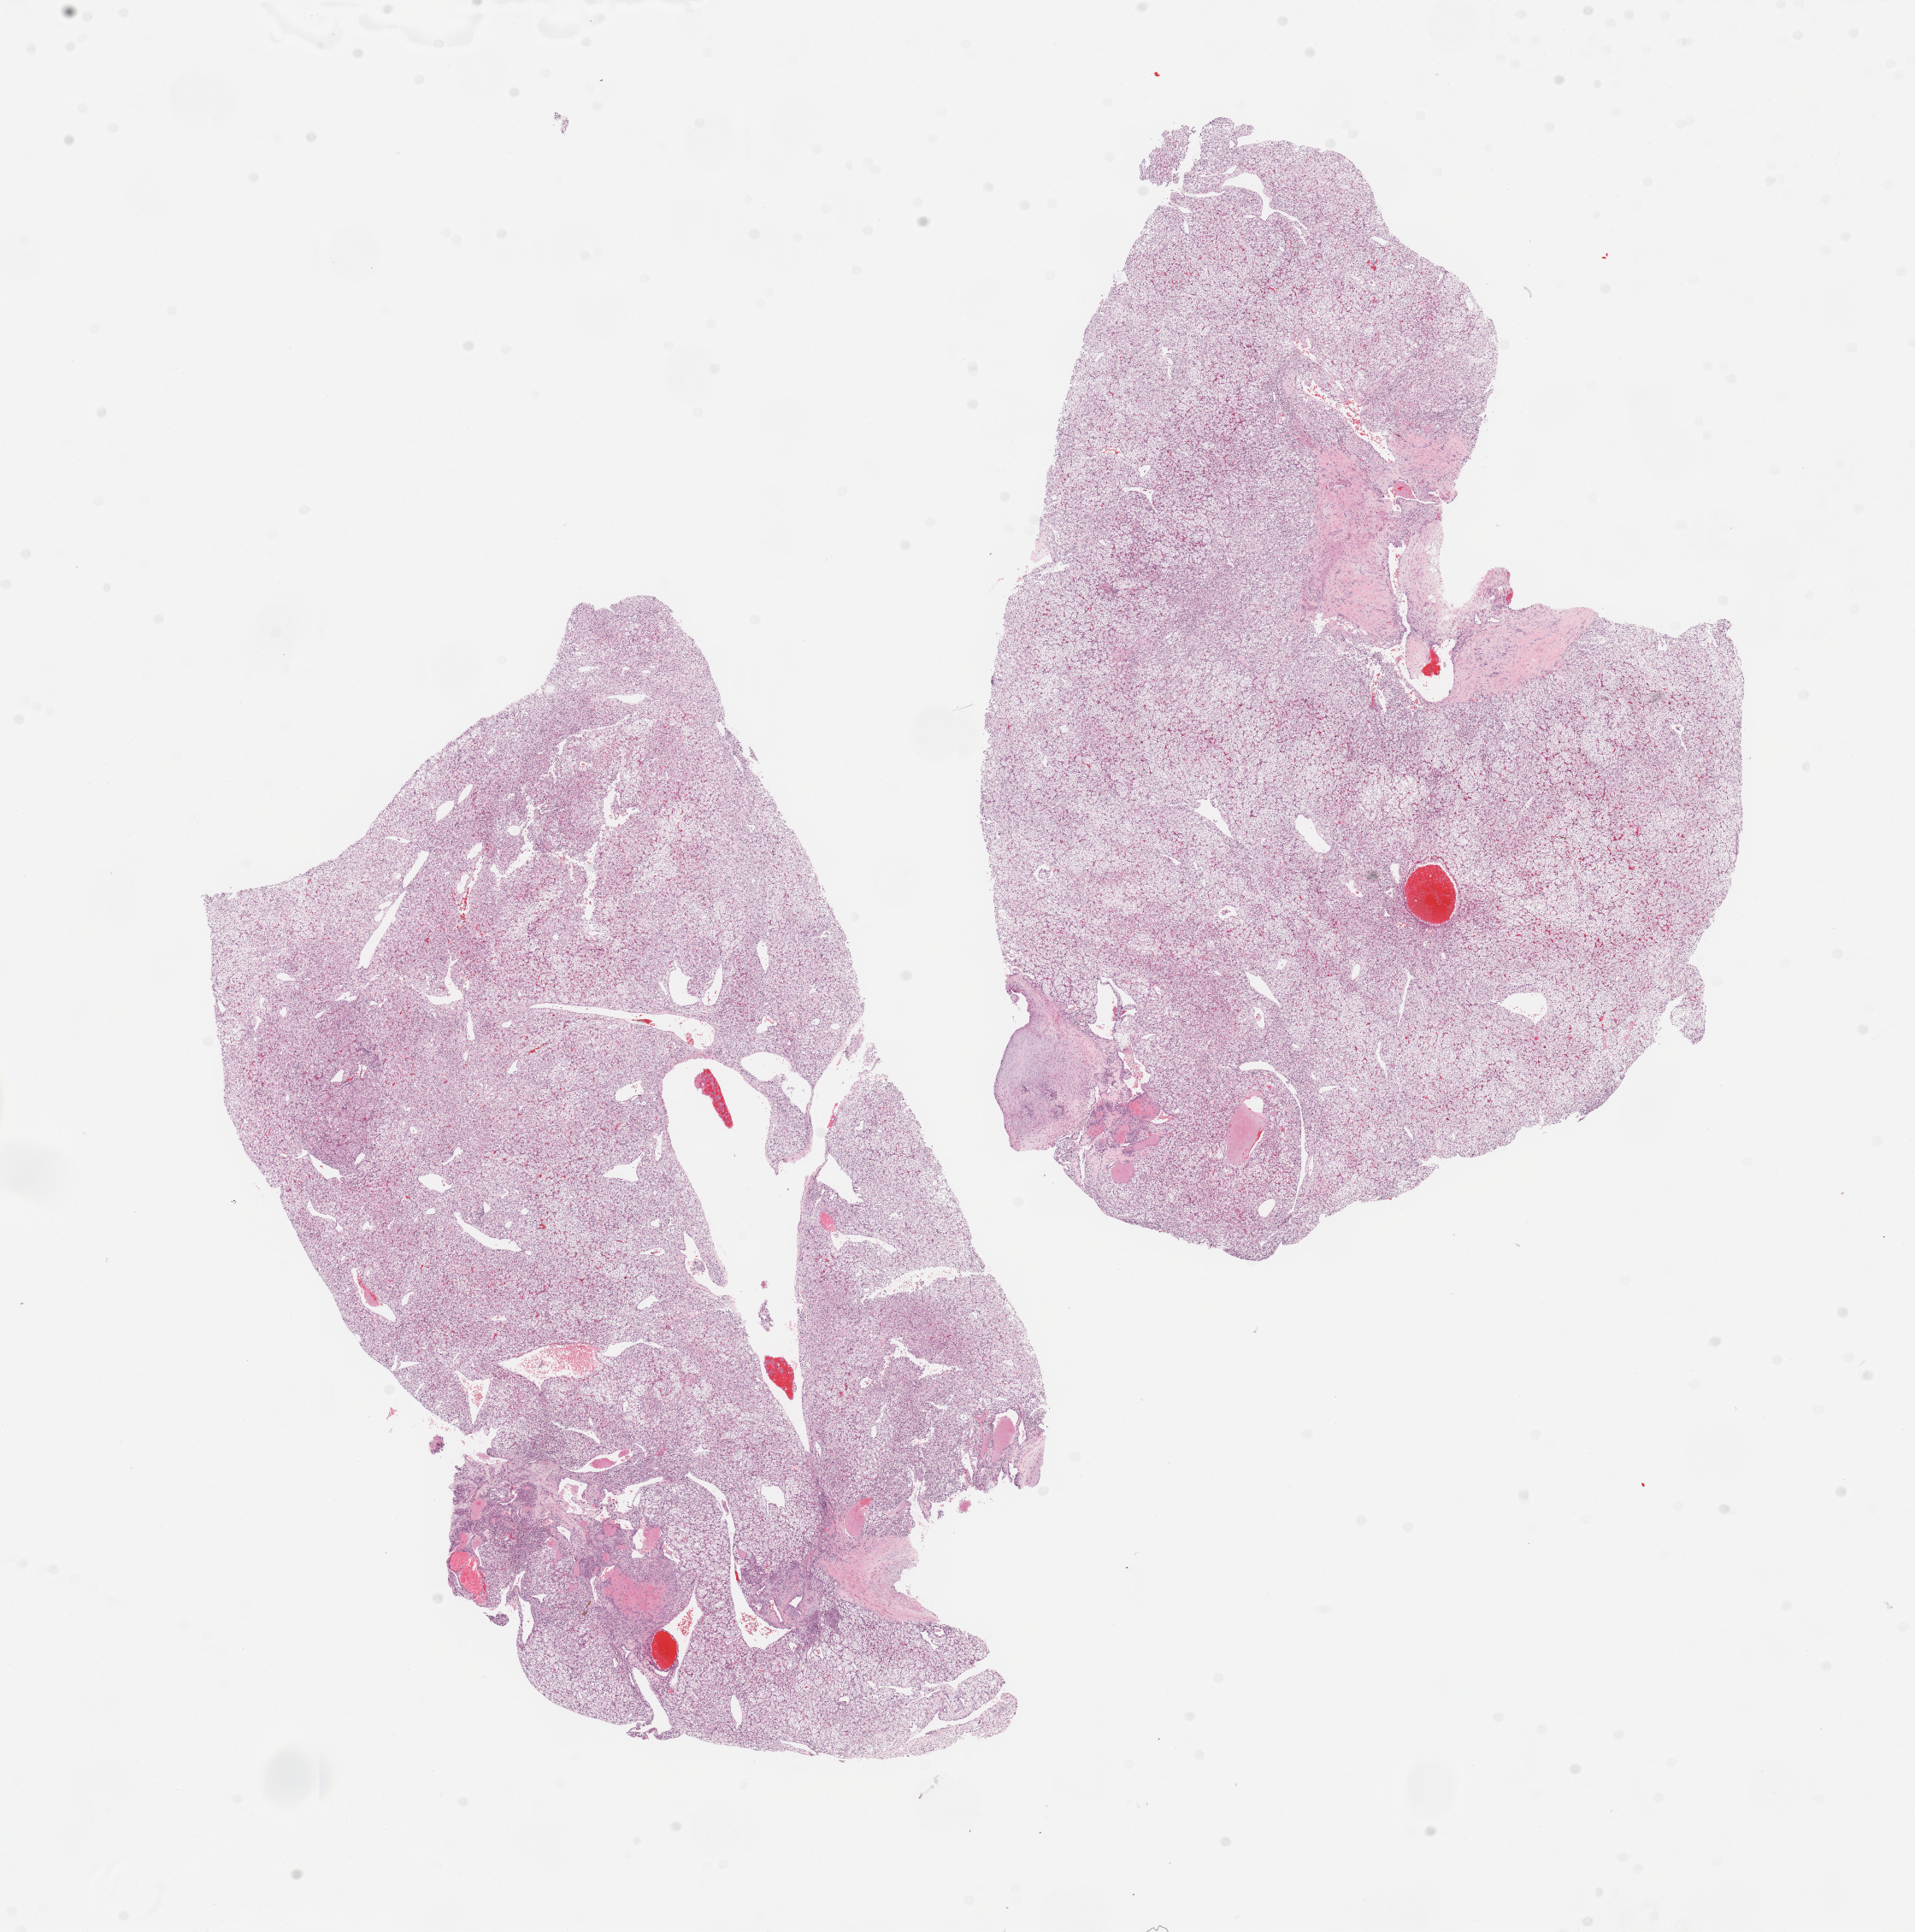
Whole-slide histology image, Hematoxylin and eosin (H&E) stained, low-resolution overview of the scanned area, about 17.7 x 17.9 mm. Tumour tissue sample, kidney. Male, 72 y/o. Histologic grade: G2 (moderately differentiated).
AJCC pathologic stage: III. Diagnosis: Renal cell carcinoma, NOS. Primary tumour site (as recorded): middle.